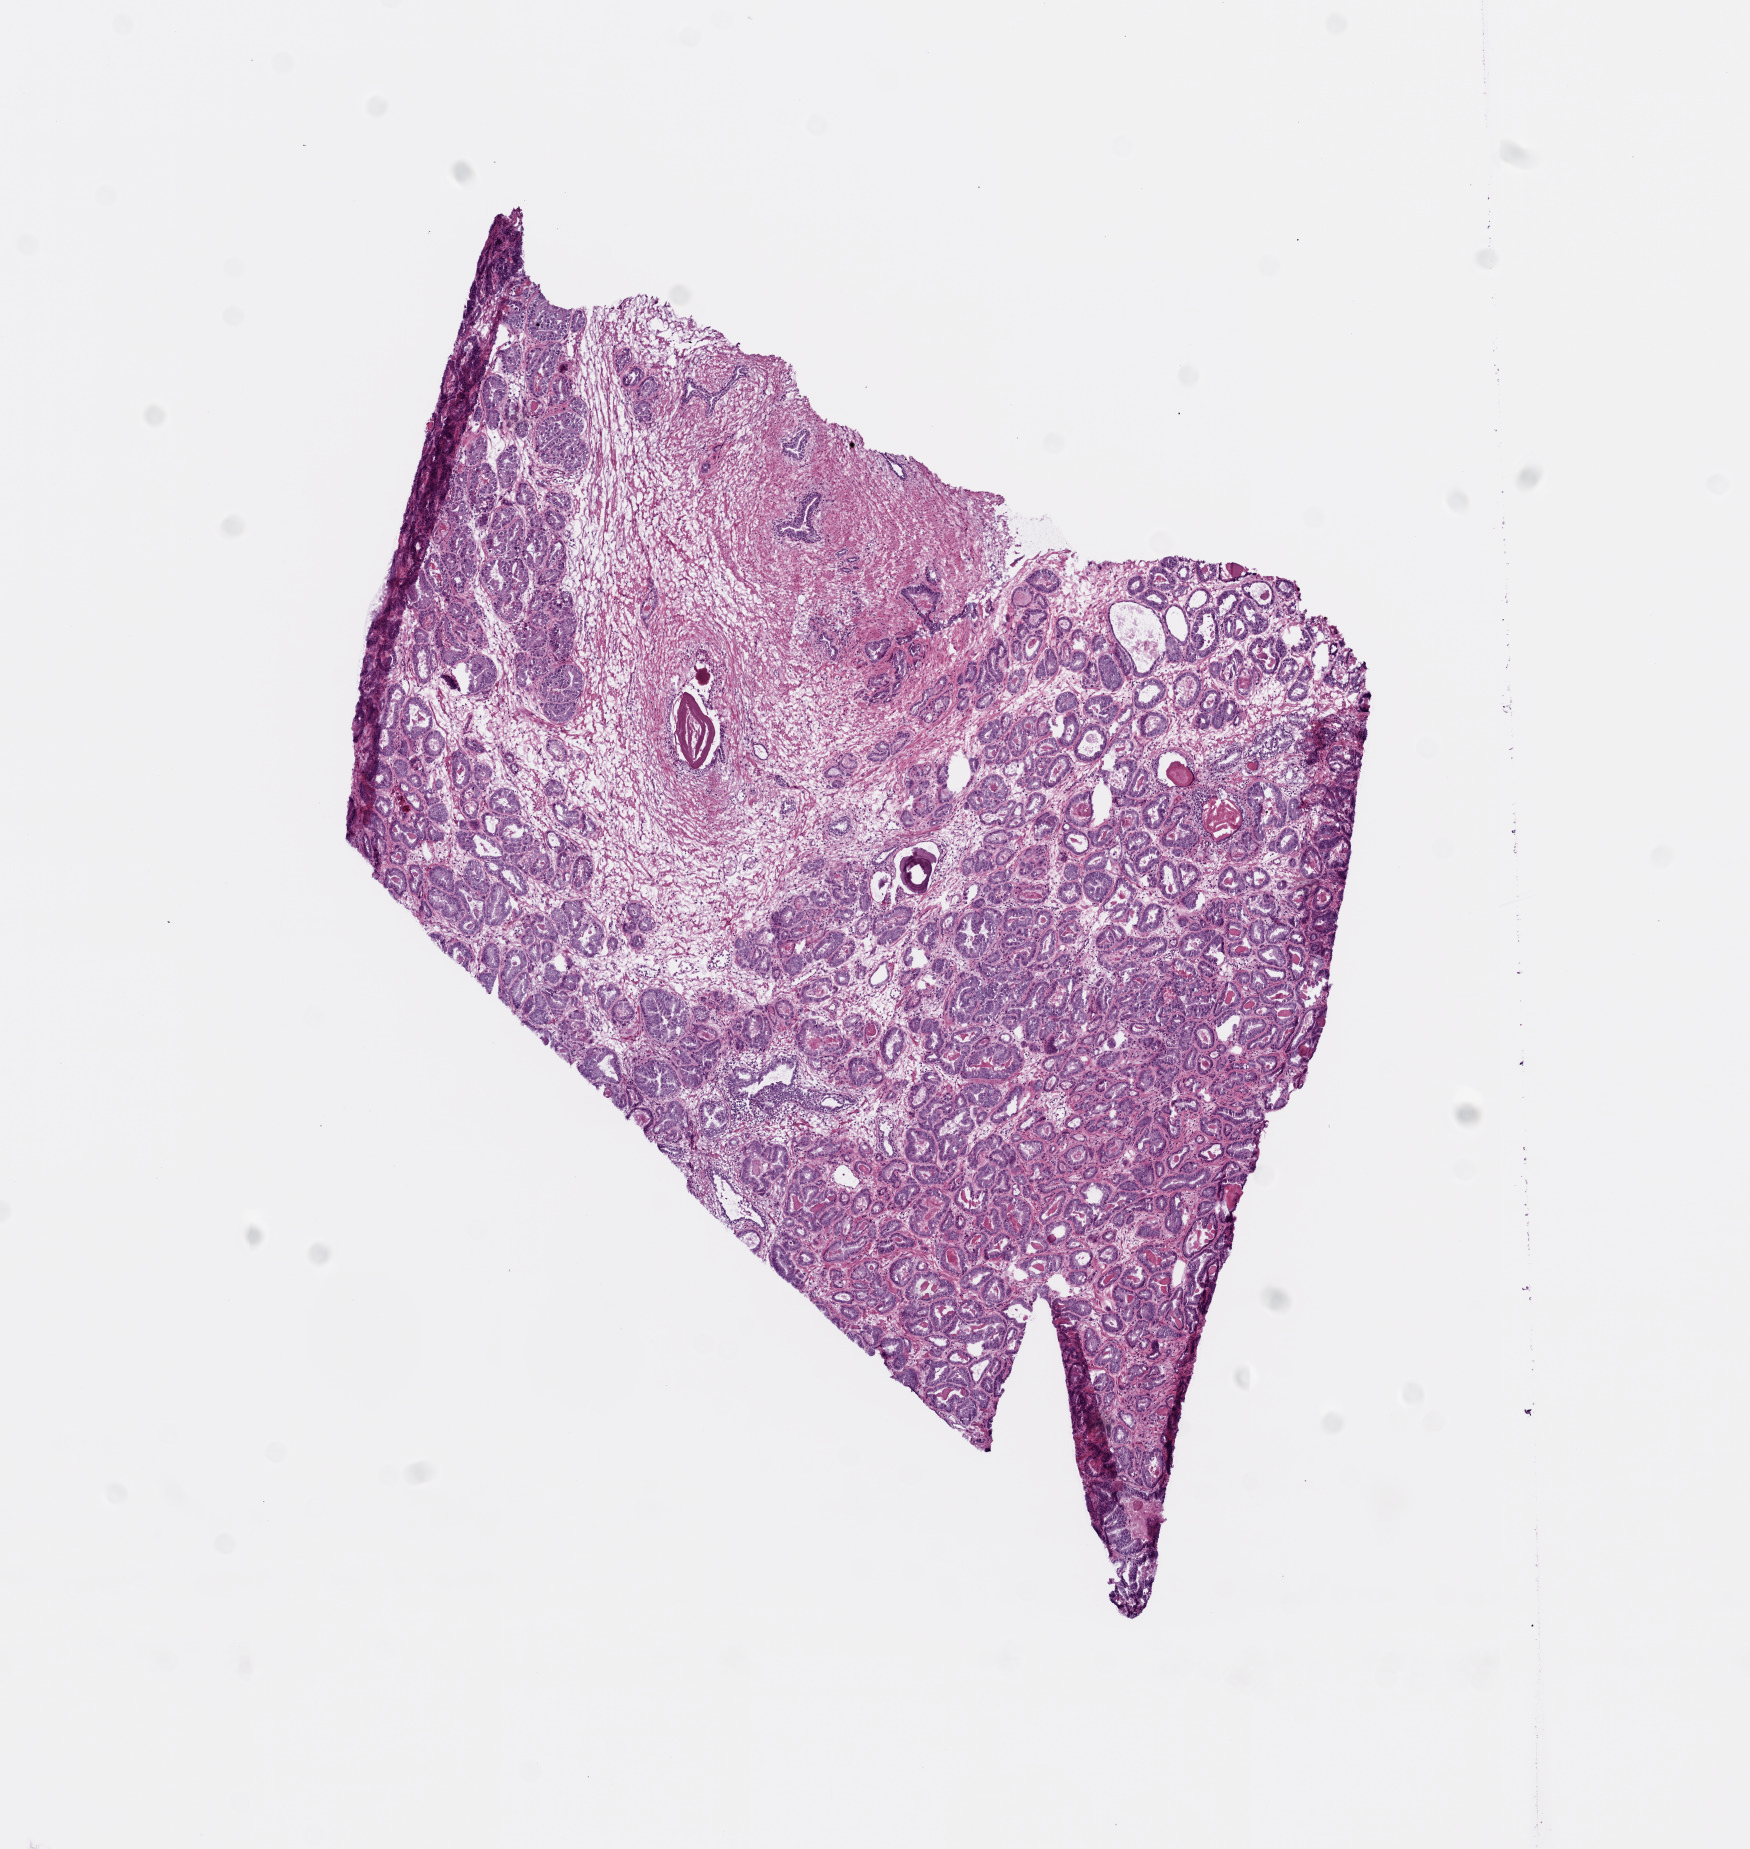
H&E whole-slide image — low-resolution overview of the scanned area, about 7.0 x 7.4 mm (from a 20x scan). Frozen section from the bottom of the tissue portion. Primary tumour sample from the prostate. Male, age 72 years at initial diagnosis. Gleason score: 7 (3+4). Pathologist review of this section (percent, as recorded): tumour cells 75%, tumour nuclei 80%, normal cells 15%, stromal cells 10%, necrosis 0%. Infiltration values recorded for this section: lymphocyte infiltration 0%, monocyte infiltration 0%, neutrophil infiltration 0%.
Diagnosis: Acinar cell carcinoma (prostate gland). Lymph nodes positive (case pathology): 0 of 7 examined. Laterality: bilateral.